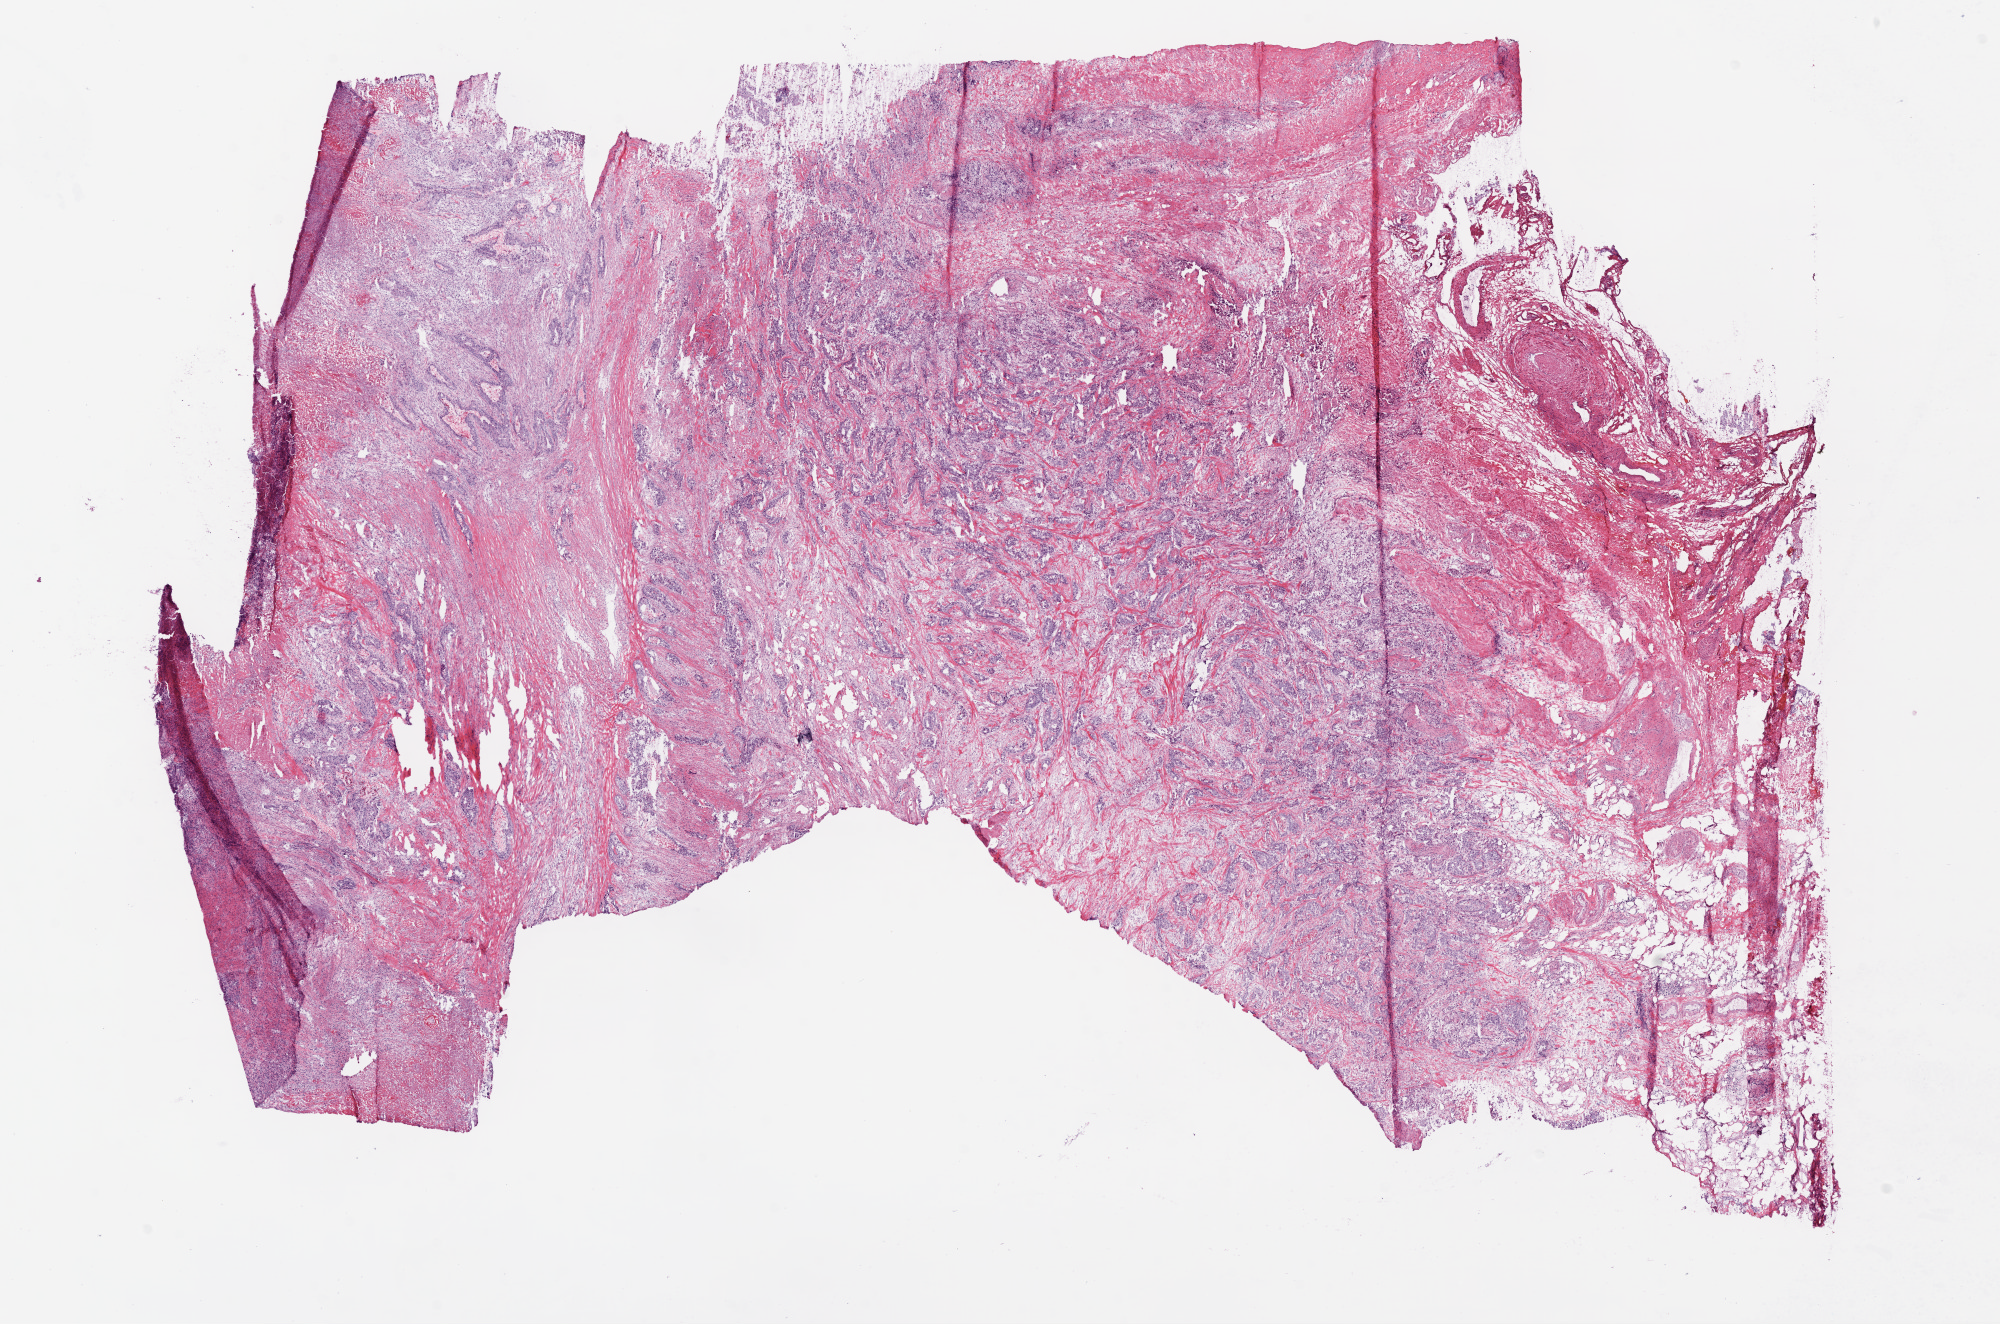
H&E-stained whole-slide image — shown as a low-resolution overview of the whole scanned area (about 16.0 x 10.6 mm), frozen section from the bottom of the tissue portion, rectum, primary tumour sample. Male, age 39 years at initial diagnosis. Composition of this section per pathologist review: tumour cells 63%, tumour nuclei 70%, normal cells 20%, stromal cells 12%, necrosis 5%.
* AJCC pathologic stage: IIIB
* diagnosis: Adenocarcinoma, NOS